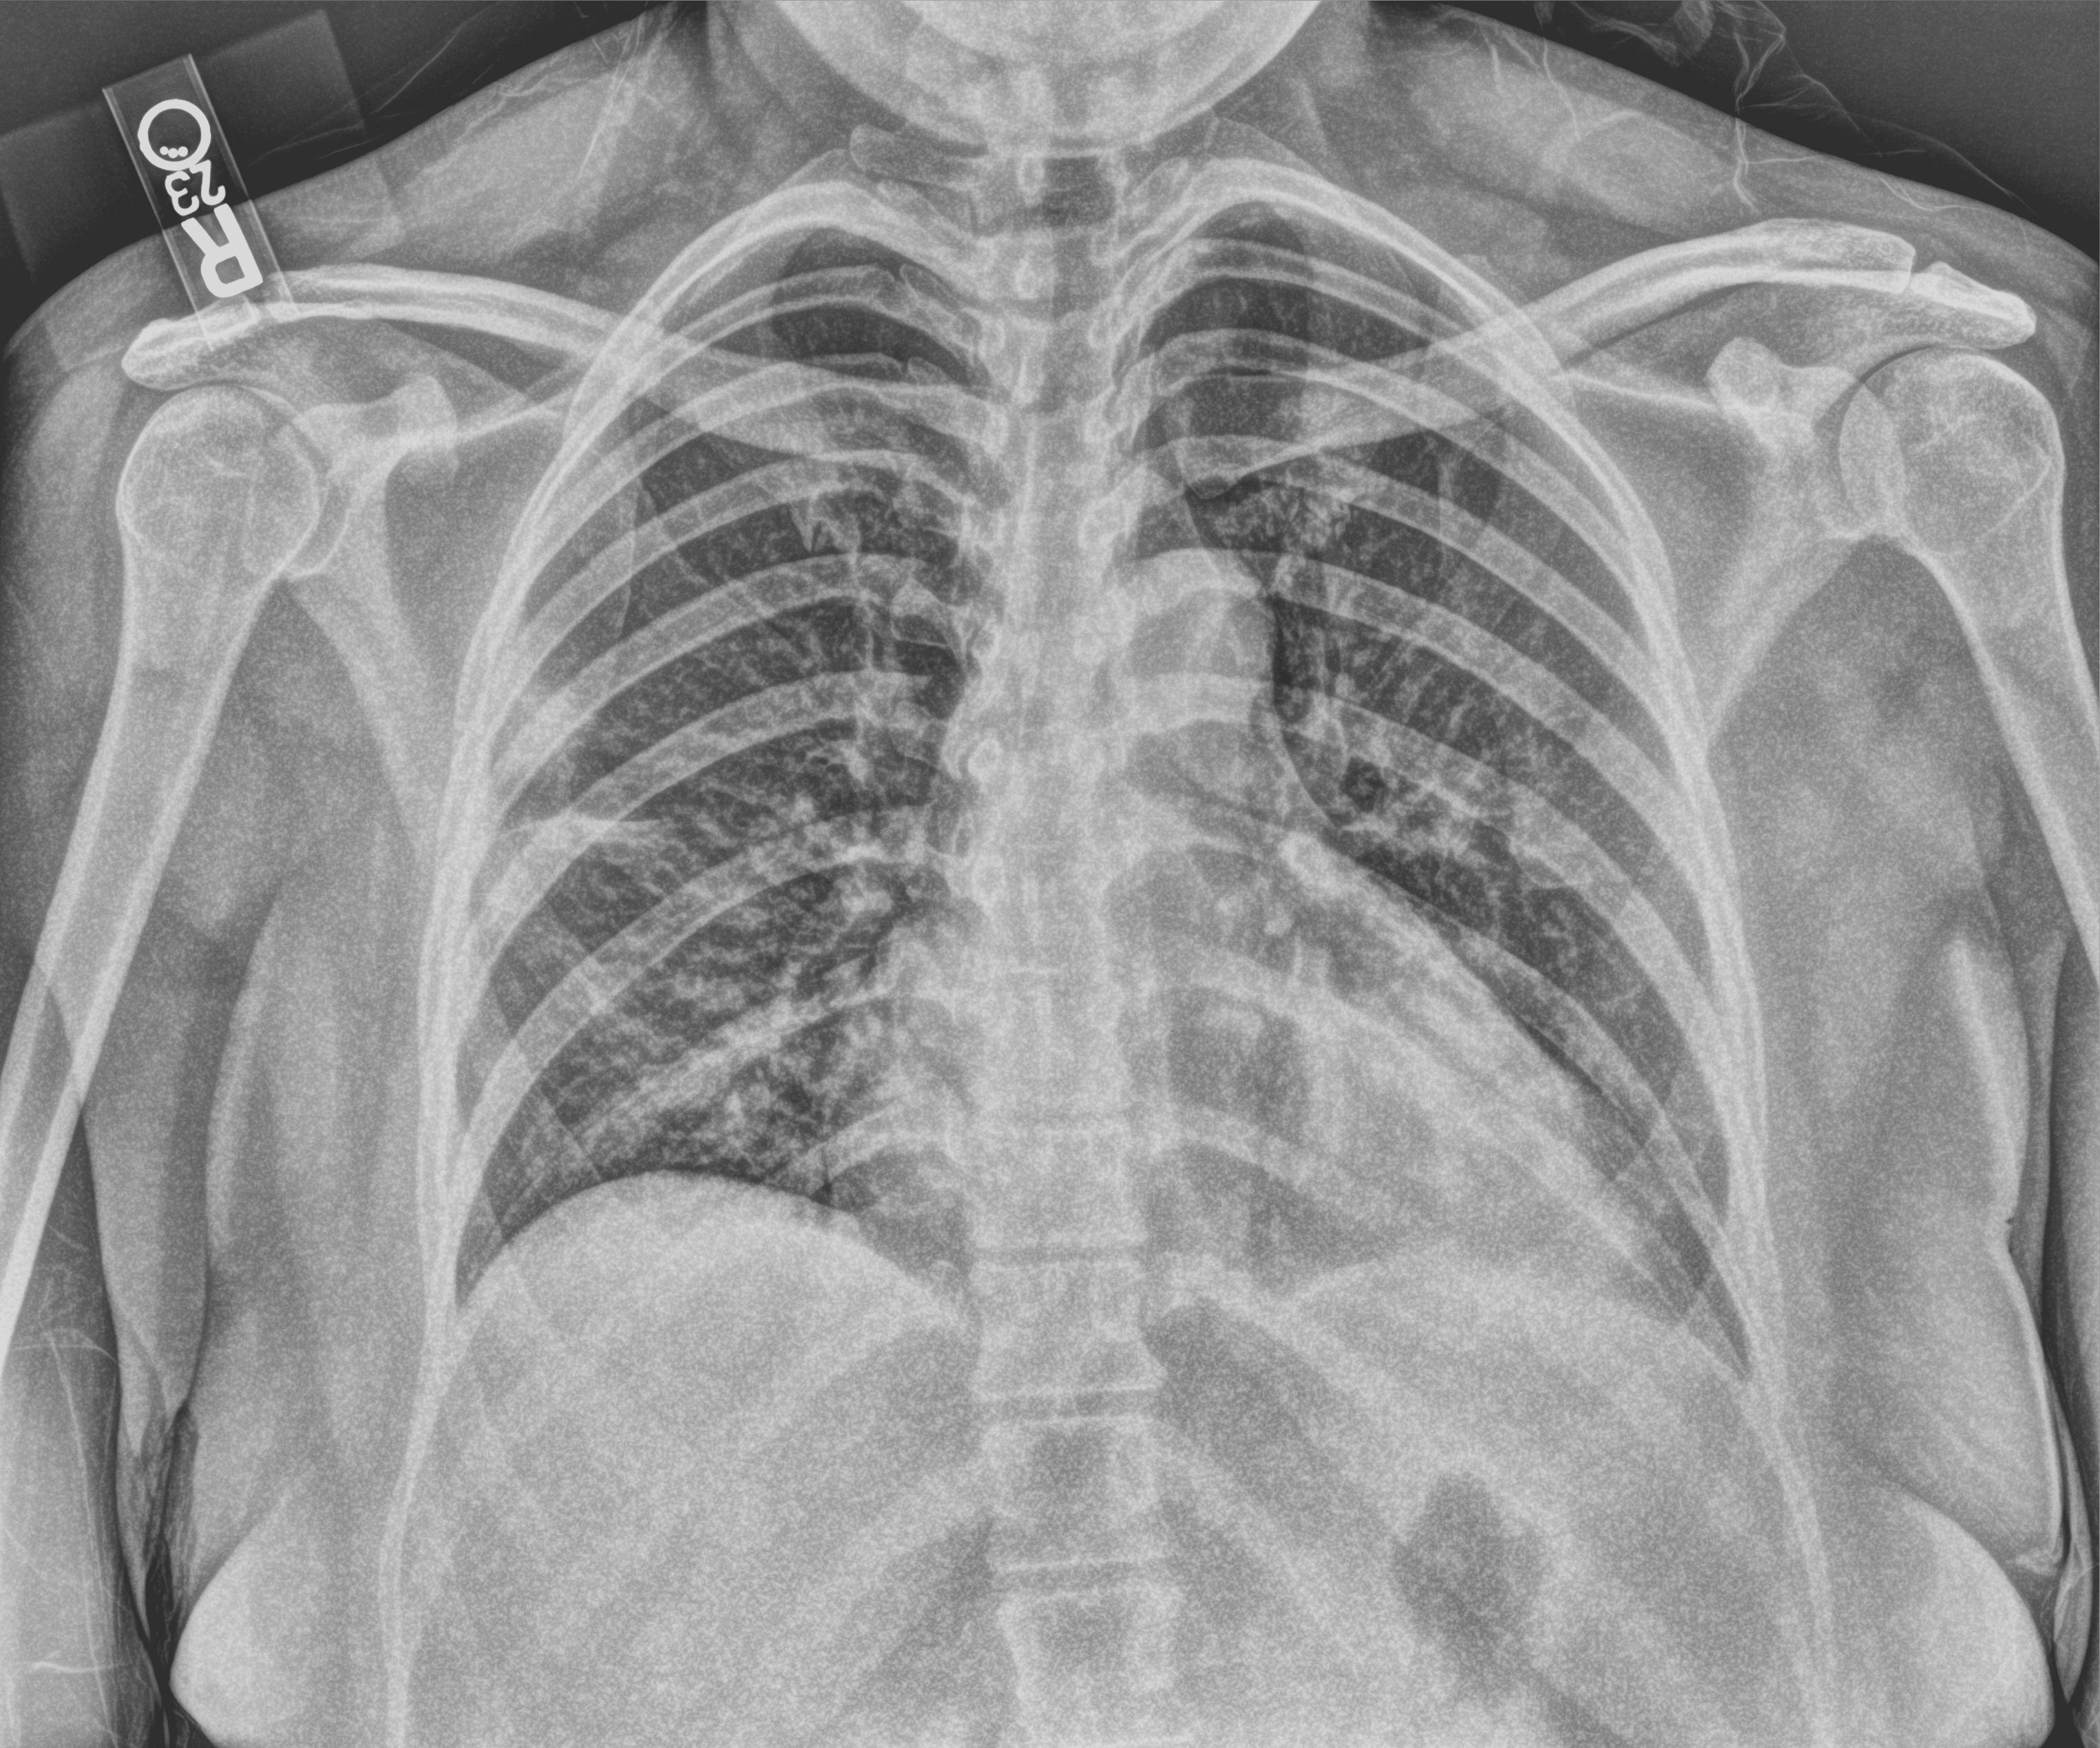
Chest X-ray (portable). Female patient hospitalised with COVID-19, age 18–59 years.
Hospital-stay facts (about this admission, not read from this image; timing relative to this image not recorded): mechanically ventilated during this hospital stay: no.